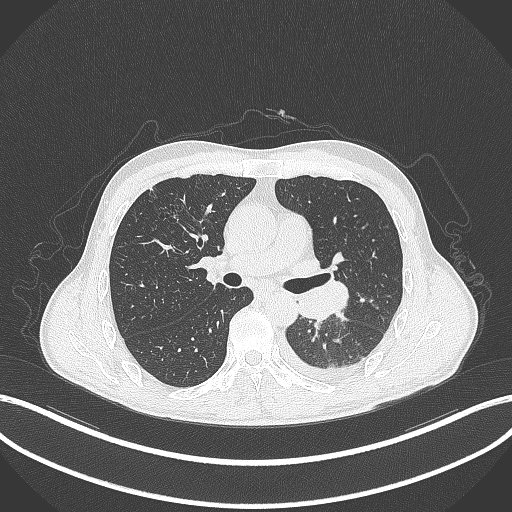
Chest CT, one axial slice. Position 189 of 295 along the scan axis. Lung window (W 1500 / L -600 HU). 512 × 512 image matrix. Patient: male, 47 years. Case-level facts recorded for this patient, not image findings: clinical TNM (as recorded): T3 N1 M1c; histopathological grade: G3.
Annotated regions visible in this slice (bounding box drawn by a radiologist):
- lung tumour (recorded histology: small cell carcinoma): box from (x=294, y=279) to (x=351, y=324) px